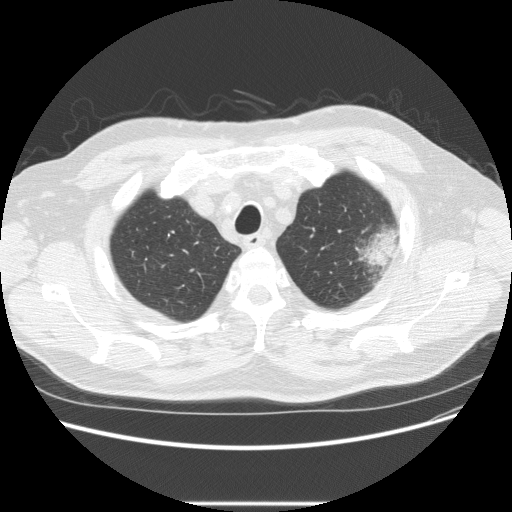
Low-dose screening chest CT, one axial slice. Position 193 of 233 along the scan axis. Reconstruction kernel STANDARD. Lung window (W 1500 / L -600 HU). 2.5 mm slice thickness. 512 × 512 image matrix, field of view 380 × 380 mm.
Annotated regions visible in this slice (manually delineated by an expert):
- lesion 1 (tumor, upper lobe of left lung): bounding box (x1, y1, x2, y2) in pixels: (357, 228, 399, 271)